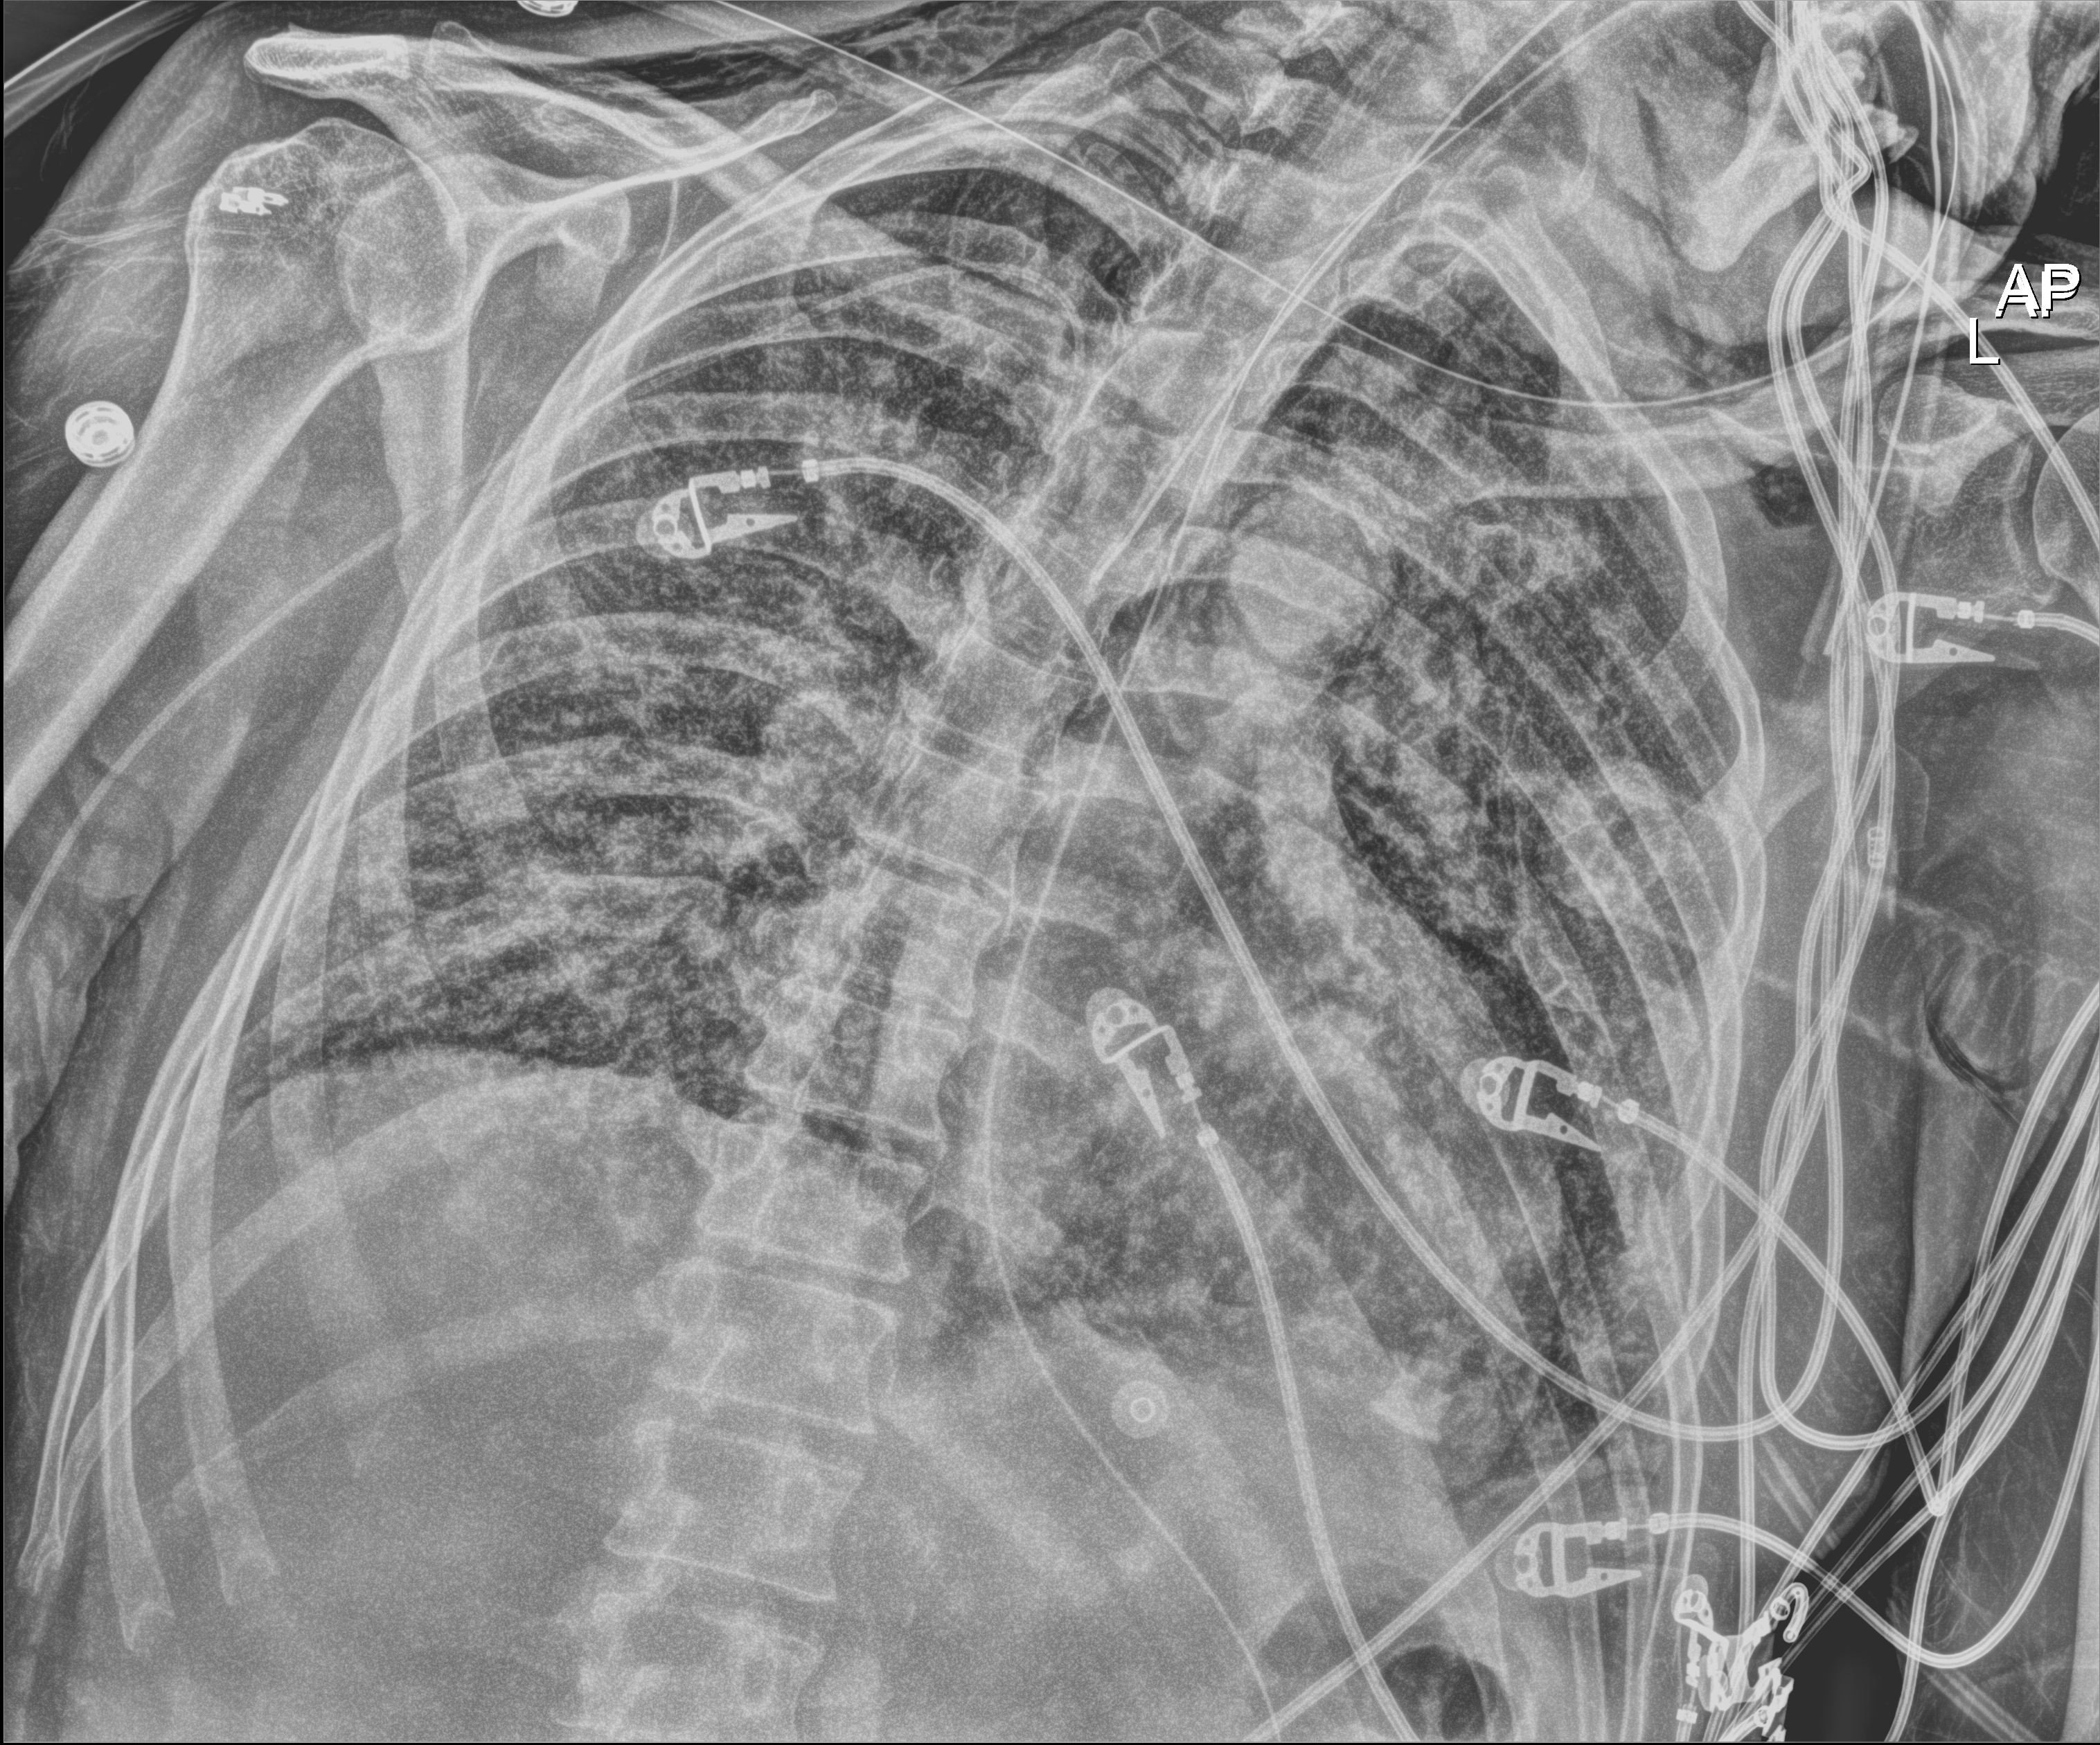
Bedside chest radiograph (digital radiography), anteroposterior (AP) projection. Patient hospitalised with COVID-19; male, aged 60–74 years.
Hospital-stay facts (about this admission, not read from this image; timing relative to this image not recorded):
- mechanically ventilated during this hospital stay: yes
- COPD (admission record): no
- hypertension (admission record): no